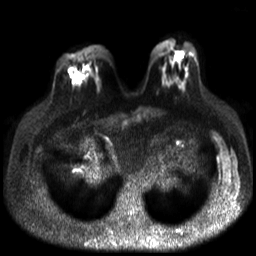
Breast MRI, one axial slice. Slice 13 of 30 in the series (ordered by position). Diffusion-weighted series; image 2 of 4 stored at this slice position (different b-values; order by instance number). 3 T. 4 mm slice thickness. 256 × 256 image matrix, field of view 320 × 320 mm. Female patient.
Annotated regions visible in this slice (expert manual segmentation):
- tumour on diffusion-weighted imaging: bounding box (x1, y1, x2, y2) in pixels: (73, 73, 81, 83)